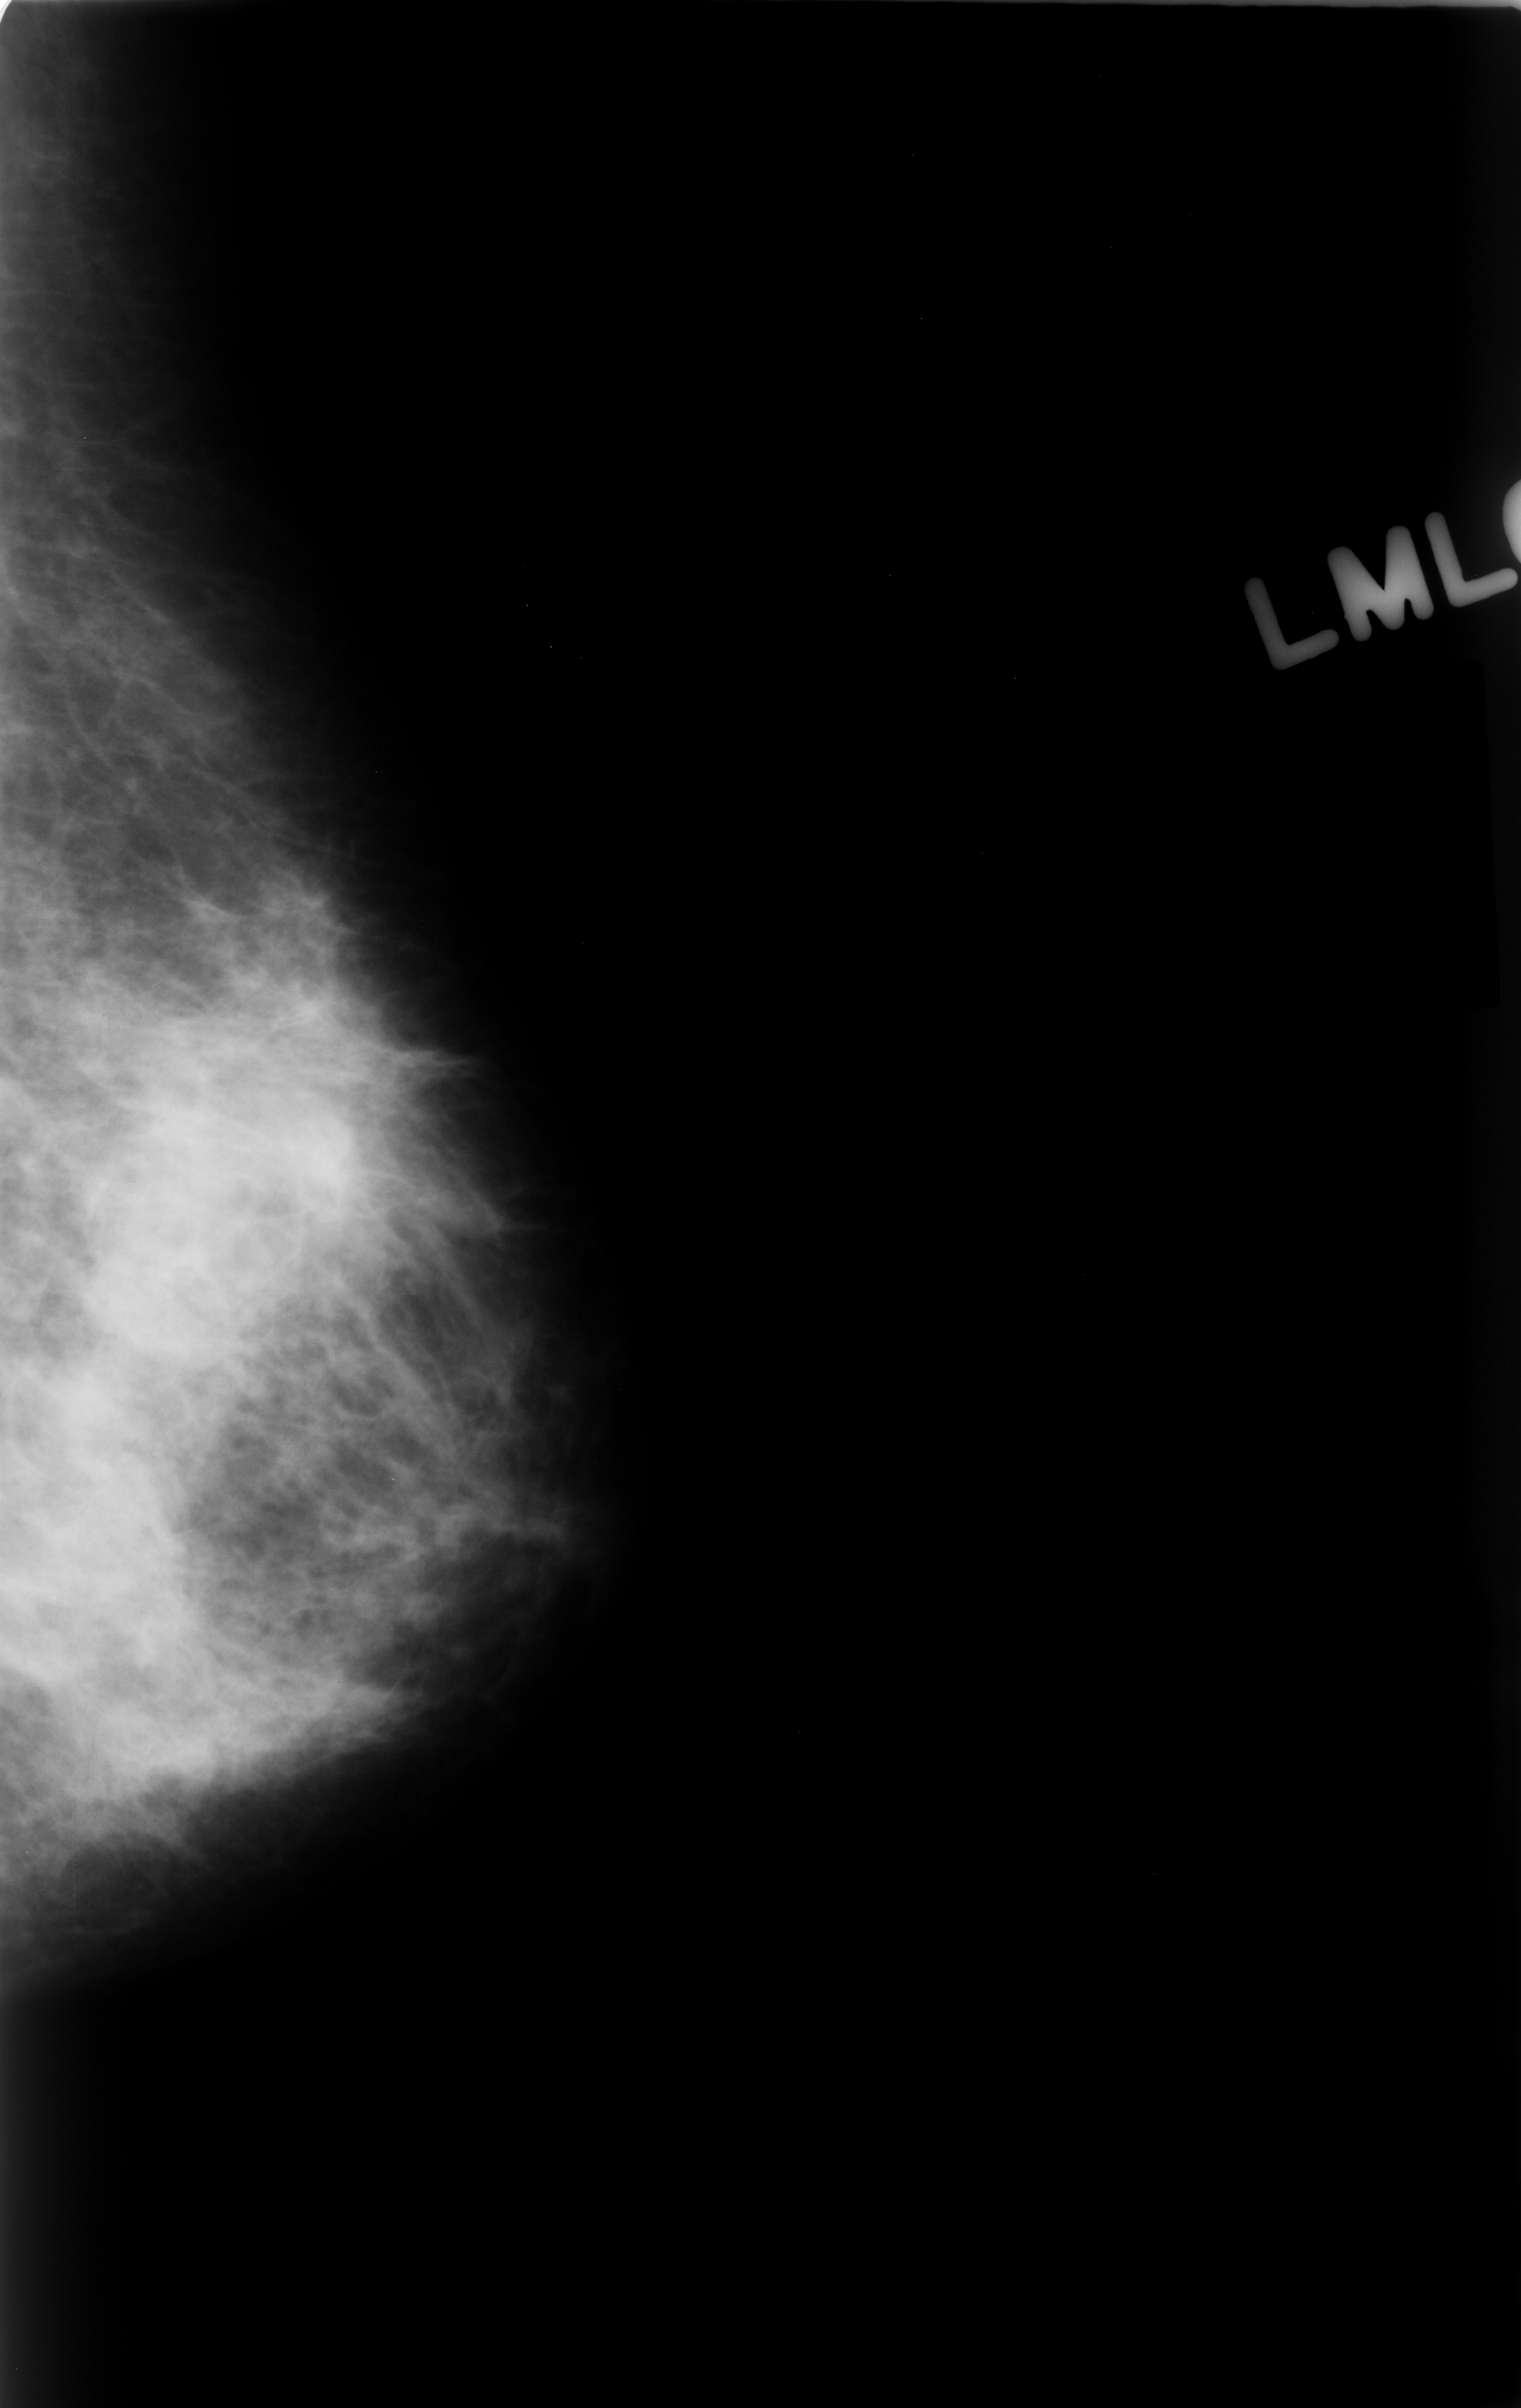
Mammogram (digitized film); left breast; mediolateral oblique (MLO) view; 1521 × 2408 image matrix.
Expert-marked regions of interest on this image (one box per marked abnormality):
- mass, shape architectural distortion, margins ill defined; BI-RADS assessment category 5; pathology result (as recorded, not read from the image): malignant: bounding box (x1, y1, x2, y2) in pixels: (51, 900, 535, 1398)